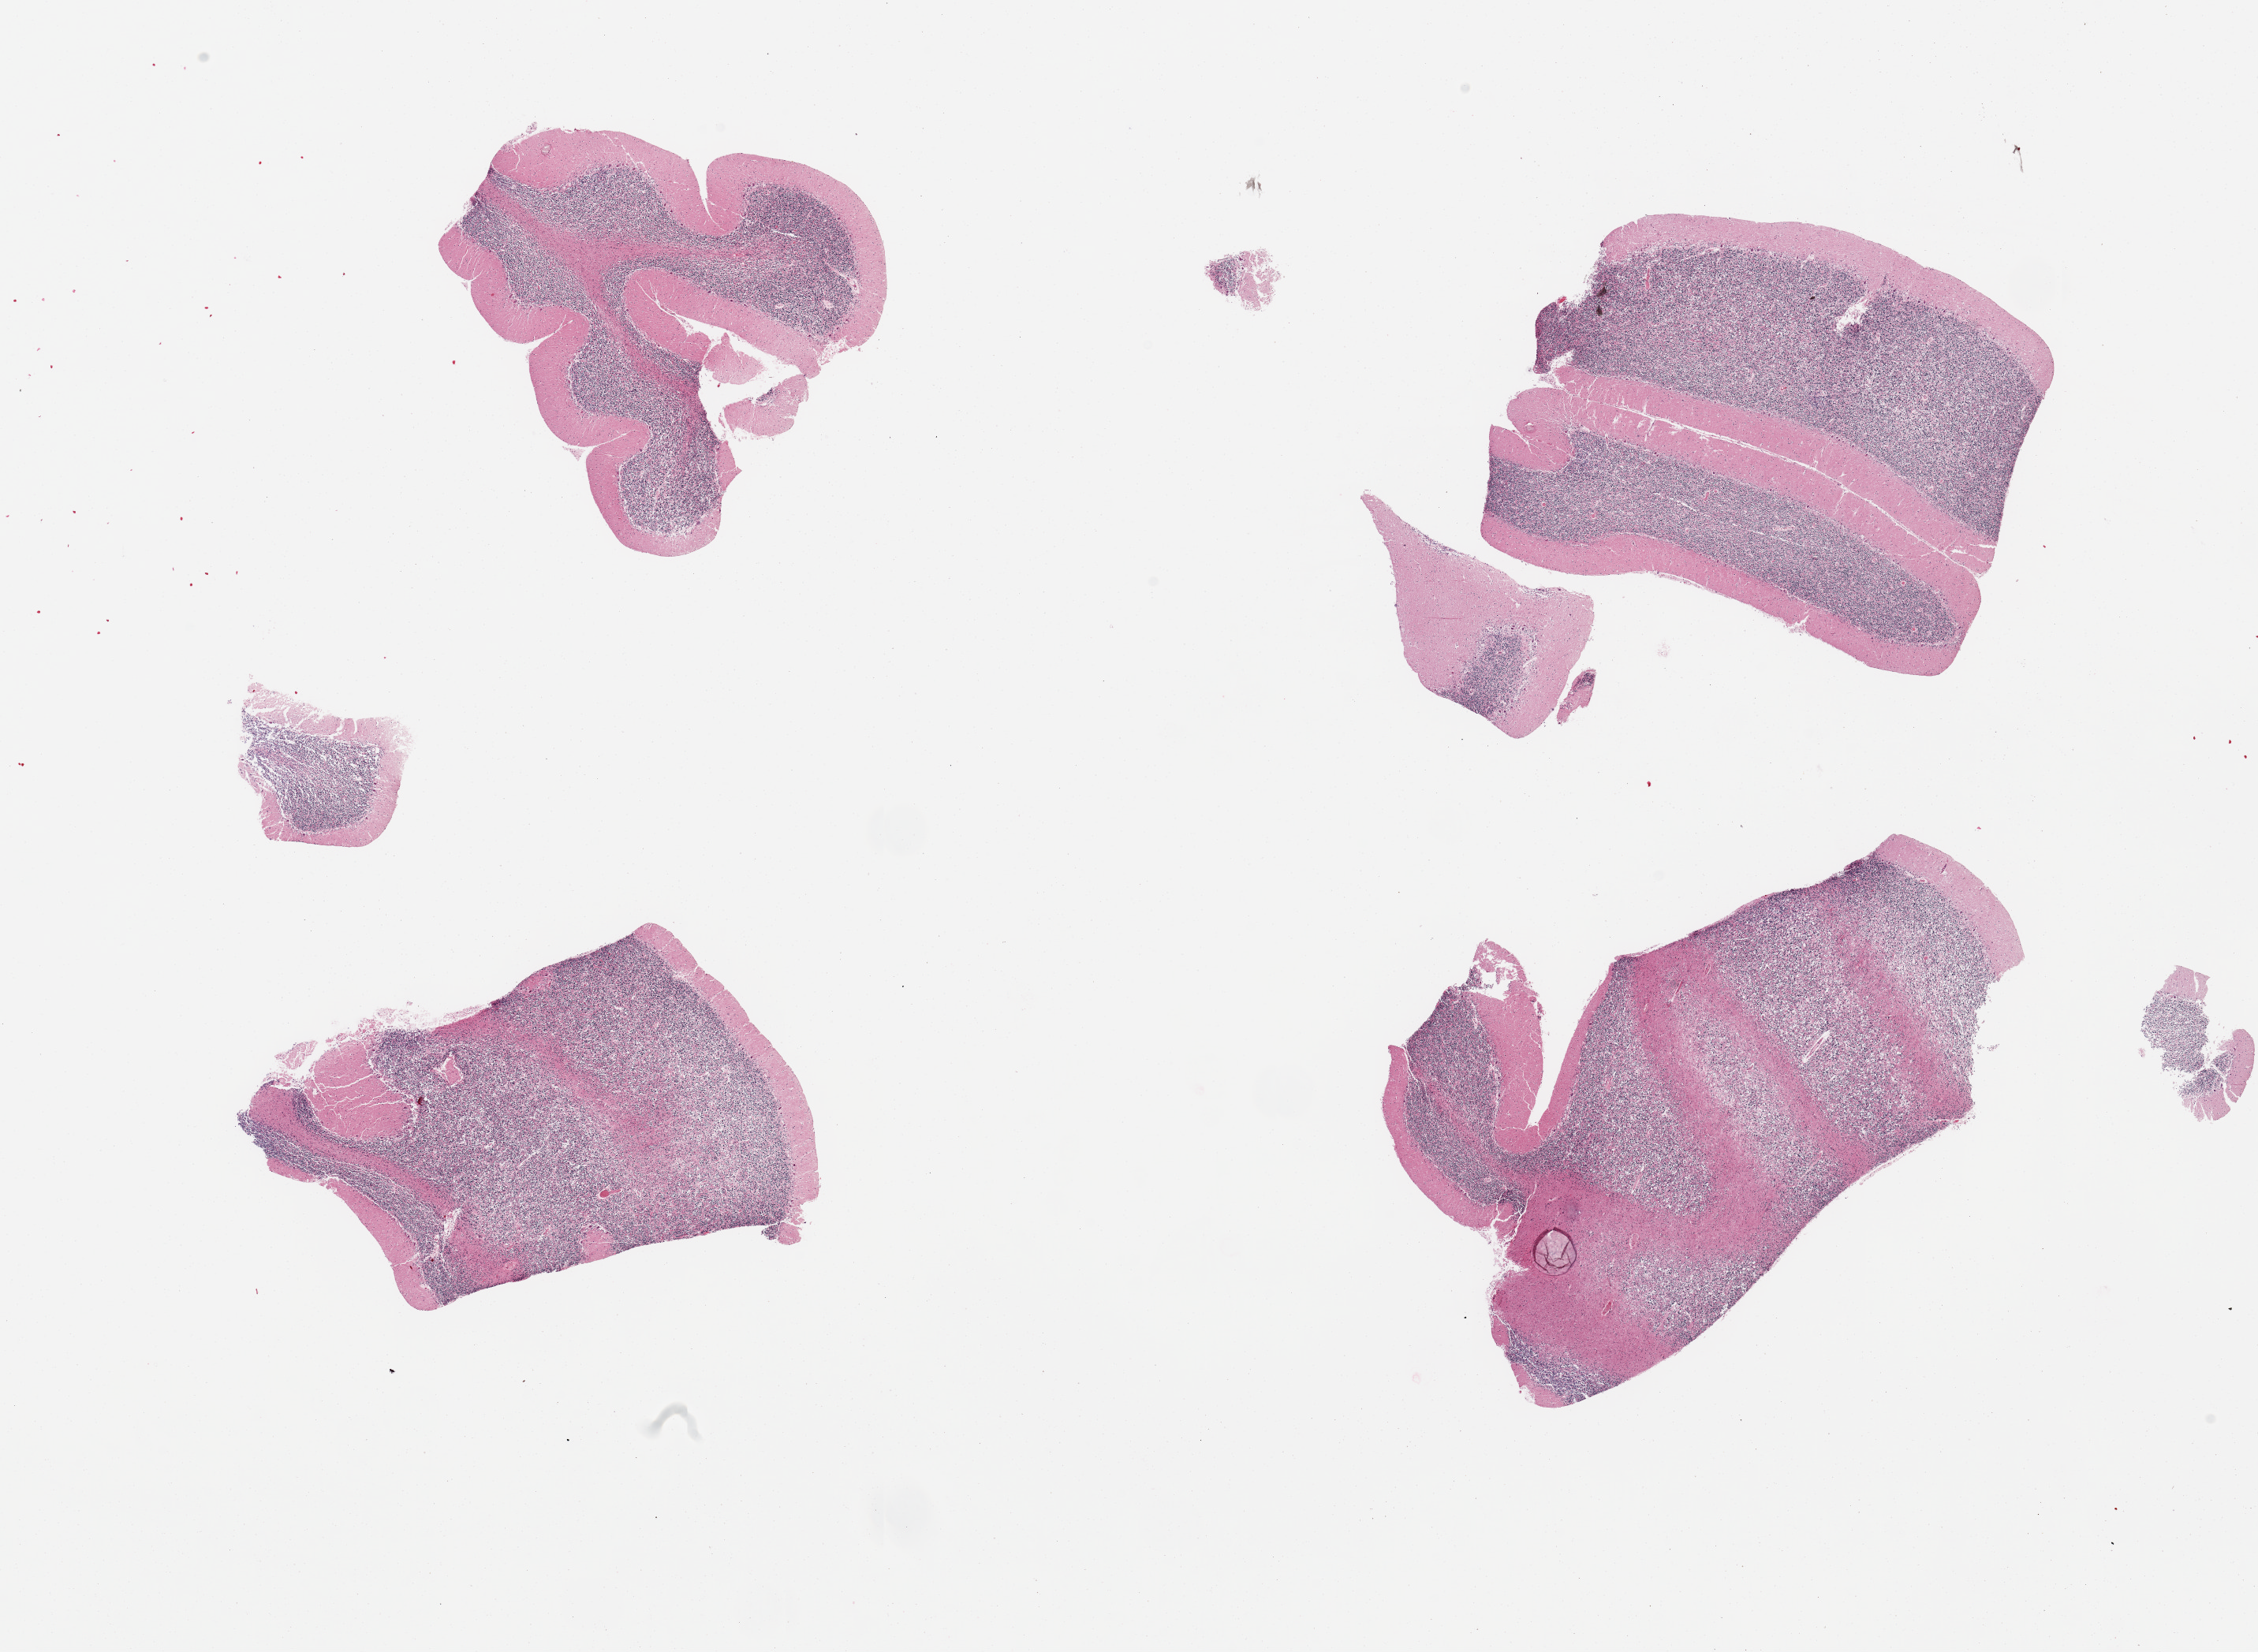
Hematoxylin and eosin (H&E) whole-slide image, brightfield, shown as a low-resolution overview of the whole scanned area (about 22.6 x 16.6 mm), PAXgene-fixed, paraffin-embedded tissue, section of cerebellum (target tissue), donor tissue sample. Male donor.
Review note (as recorded): 4 pieces (fragmented), no abnormalities.